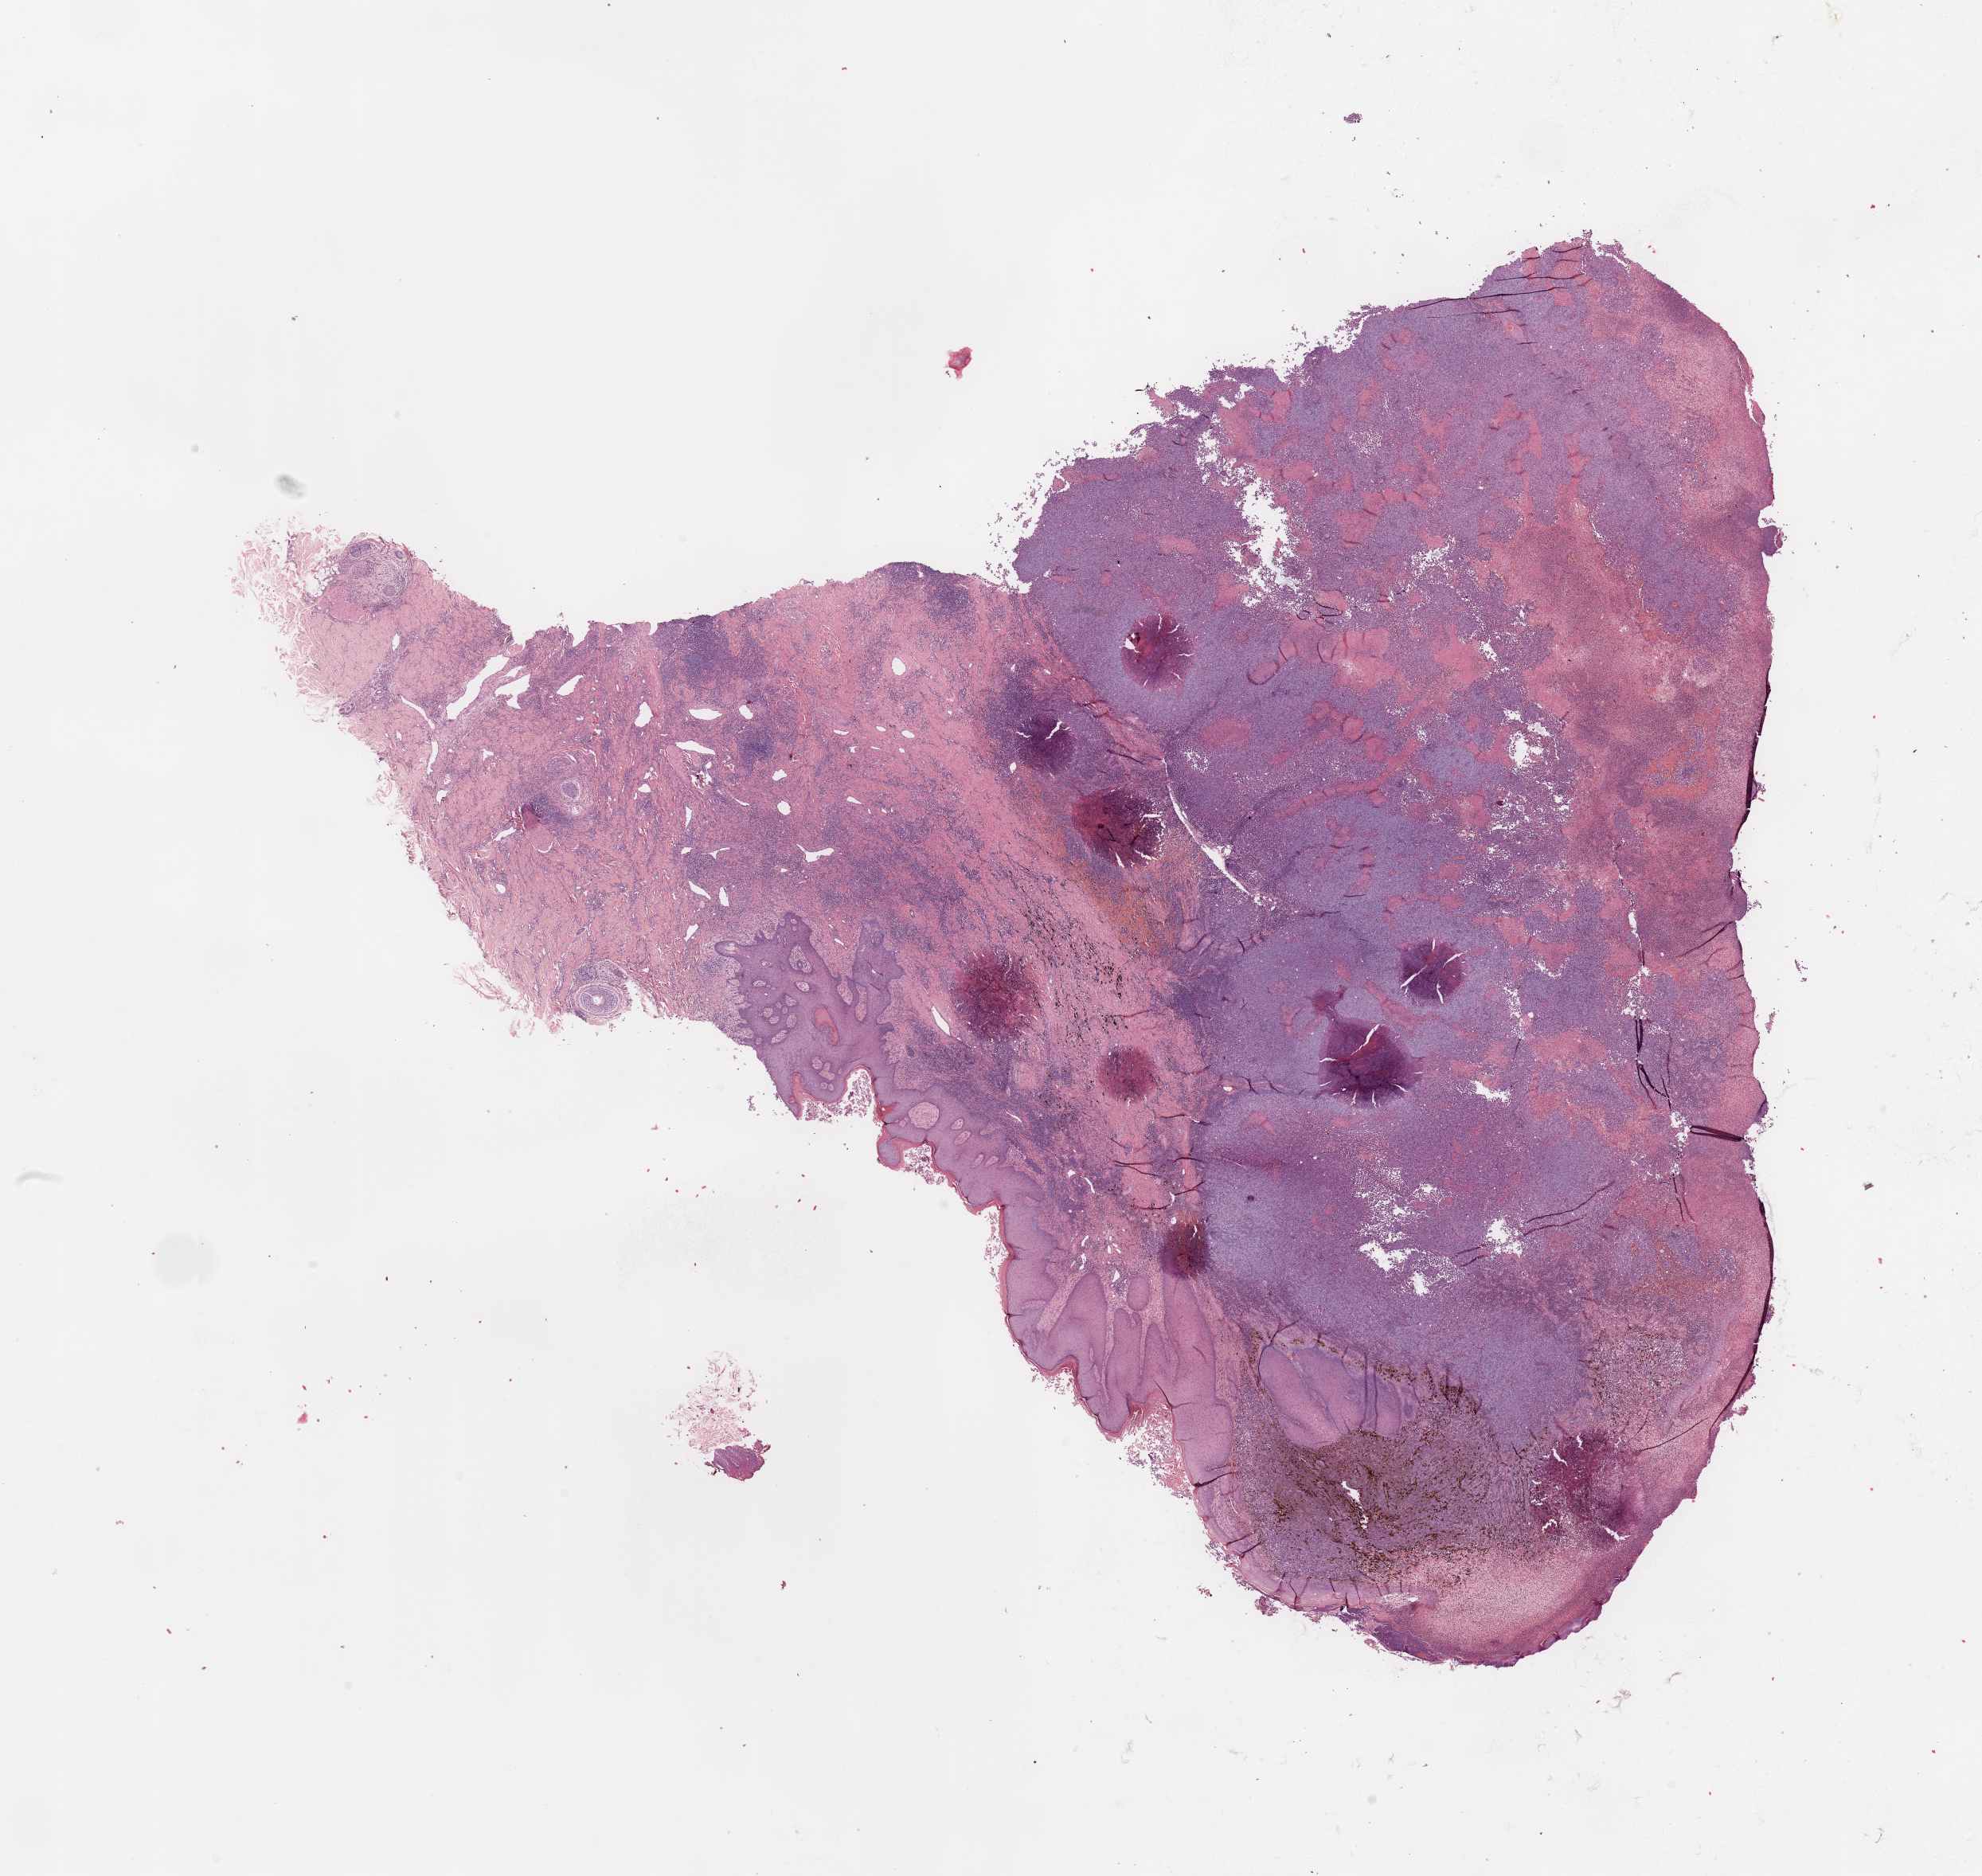
Digitized Hematoxylin and eosin (H&E) stained tissue section (whole slide), a low-resolution overview of the entire scanned area, about 19.7 x 18.6 mm (slide scanned at 20x), melanoma tumour tissue; sampled site not recorded. Male, 57 y/o.
* primary tumour site (as recorded): trunk
* AJCC pathologic stage: IIC
* diagnosis: Malignant melanoma, NOS